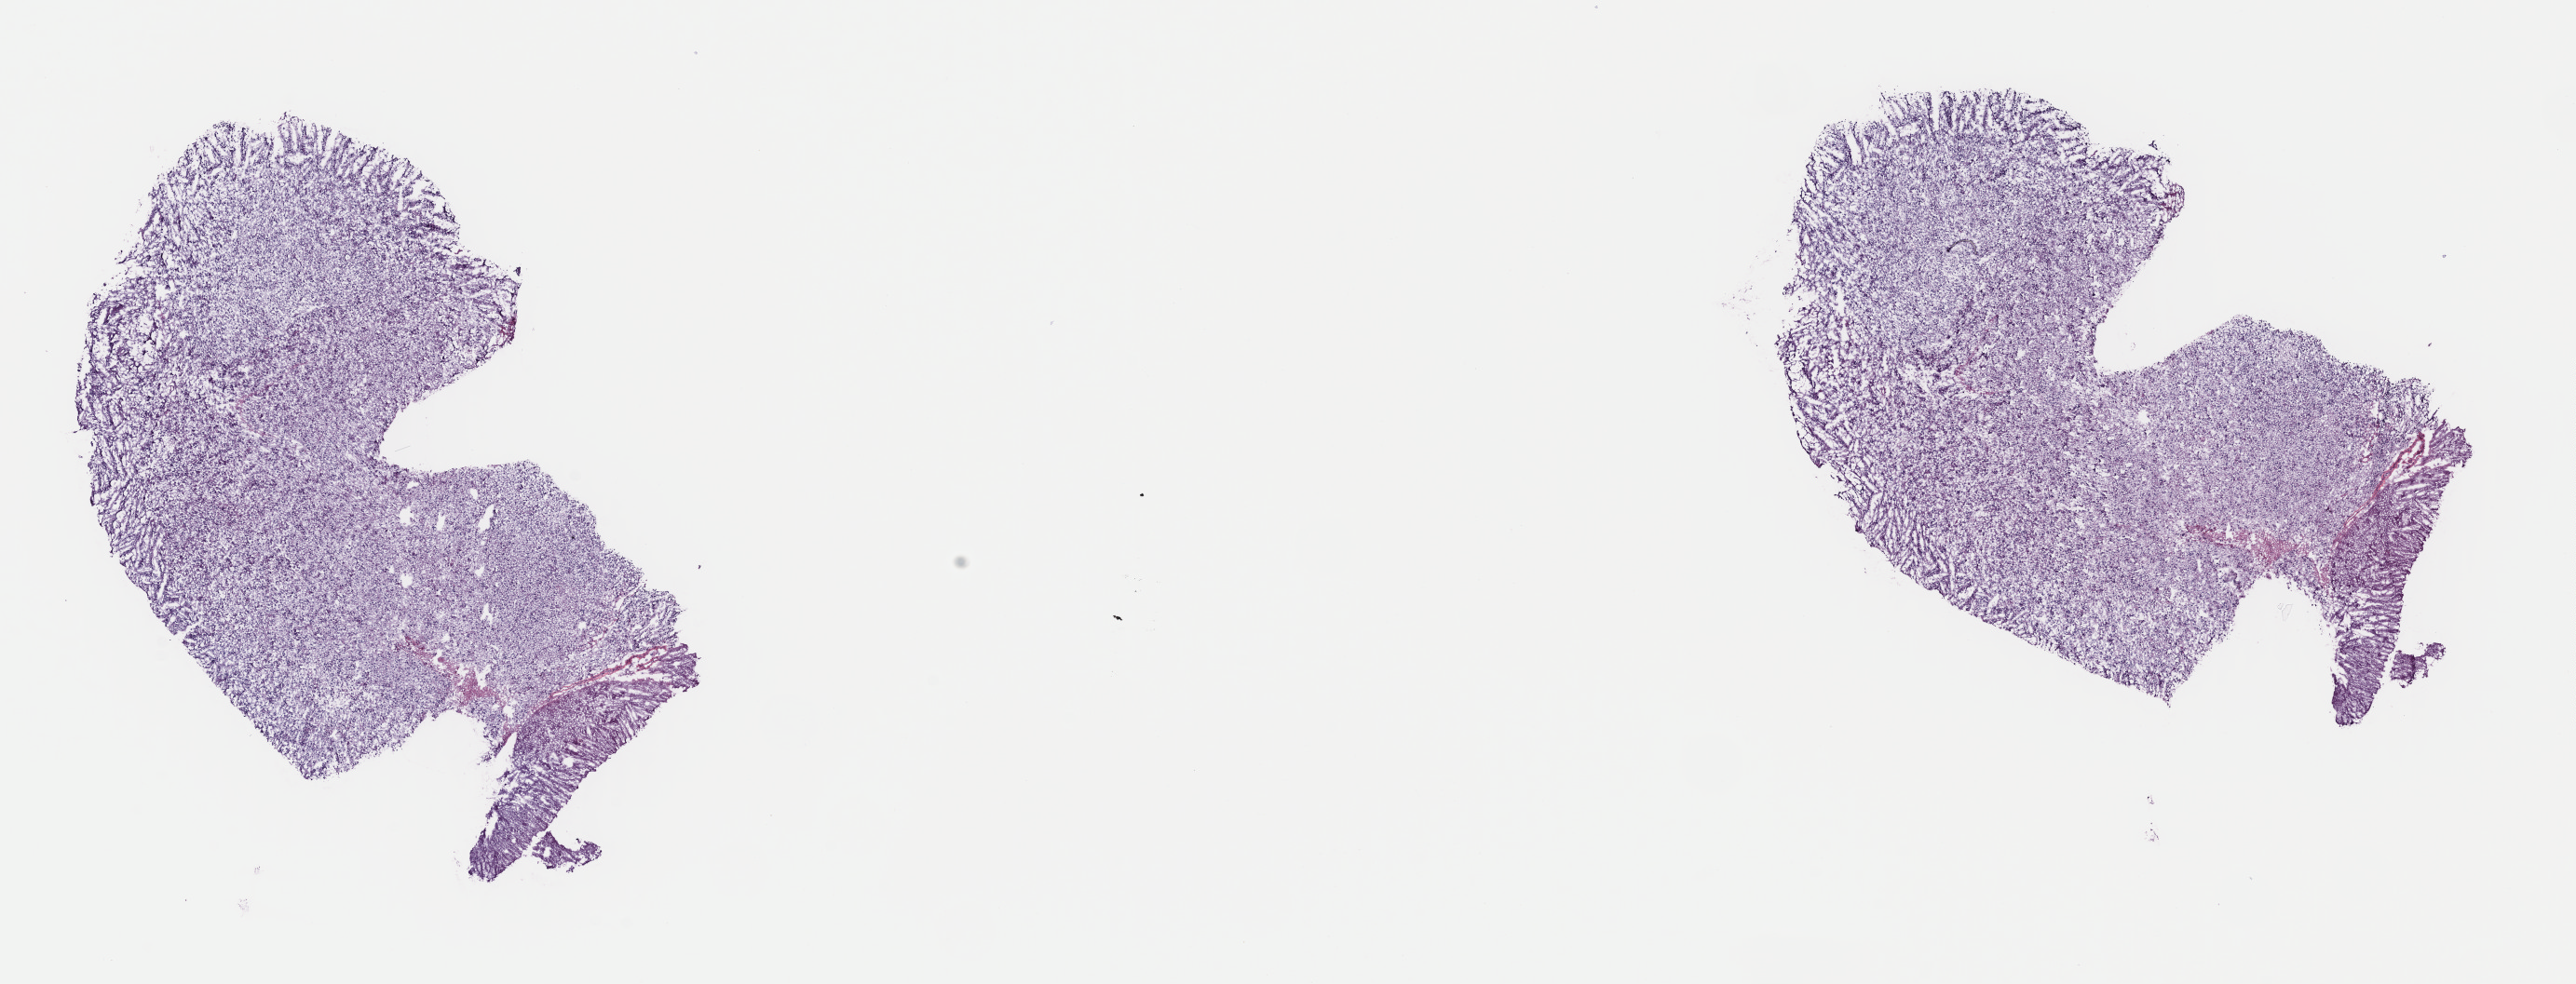
Digitized H&E-stained tissue section (whole slide) — low-resolution overview of the scanned area, about 21.8 x 8.3 mm (acquisition: 40x scan). Frozen section from the top of the tissue portion. Primary tumour sample from the brain. Patient: male, age at initial diagnosis 60 years. Histologic grade: G2 (moderately differentiated). Slide review estimates, as recorded: tumour cells 60%, tumour nuclei 85%, normal cells 10%, stromal cells 30%, necrosis 0%. Inflammatory infiltration, as recorded: lymphocyte infiltration 0%, monocyte infiltration 0%, neutrophil infiltration 0%.
Diagnosis: Oligodendroglioma, NOS (cerebrum). Laterality: right.